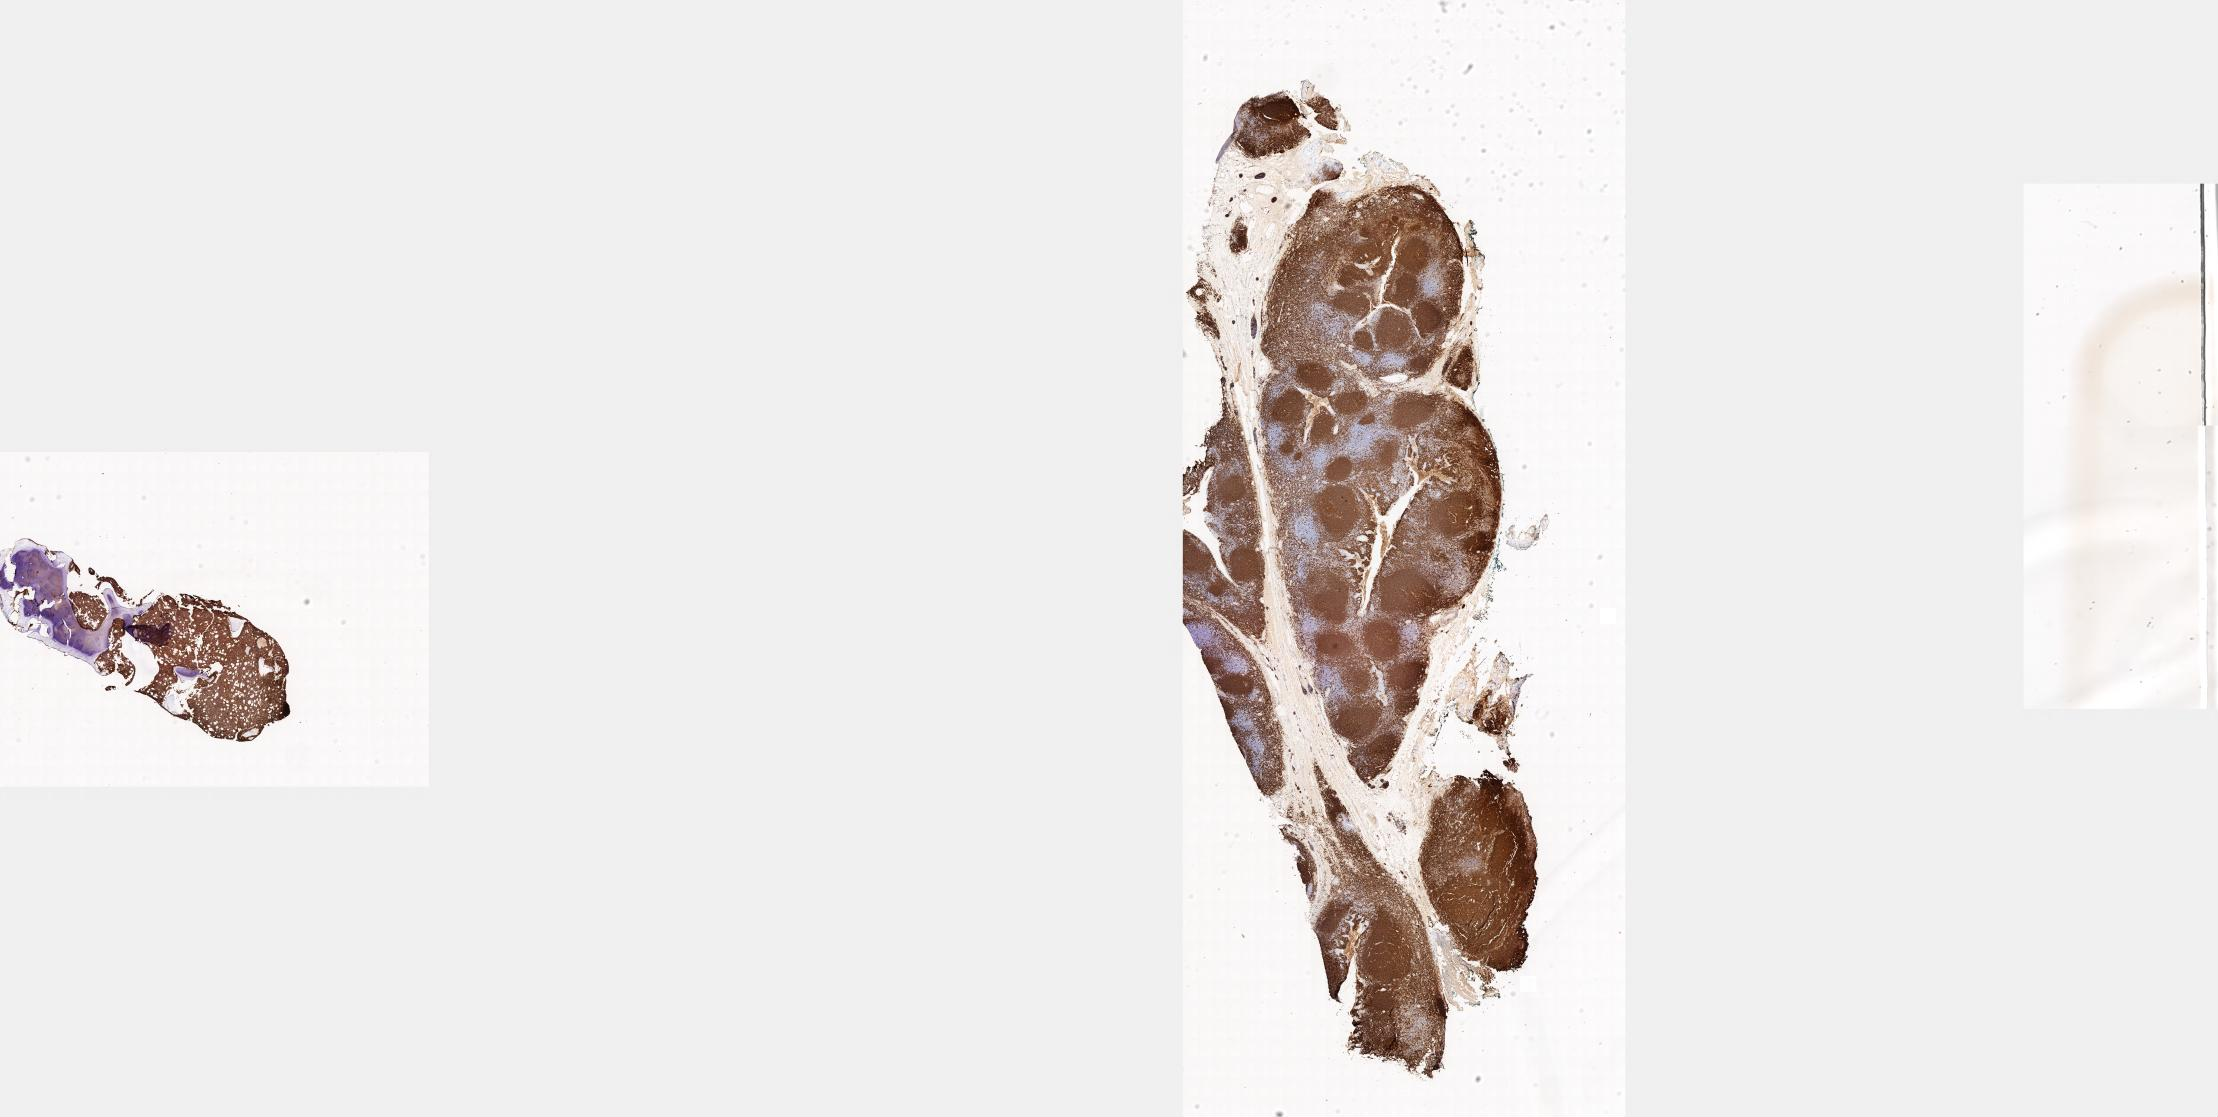
IHC for CD20, whole-slide image, whole scanned area shown as a low-resolution overview; tumor tissue; anatomic site: bone marrow. Patient male; 15 years old.
- diagnosis: Burkitt lymphoma, NOS